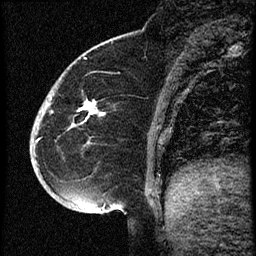
Breast MRI (dynamic contrast-enhanced), one sagittal slice; position 17 of 60 along the scan axis; dynamic contrast-enhanced study with each time point stored as its own series, time point 2 of 3 at this slice position (early post-contrast, ordered by acquisition time); 1.5 T; TE 4.2 ms, TR 18.9 ms; 256 × 256 image matrix, field of view 200 × 200 mm. Female patient. Case-level facts recorded for this patient, not image findings: setting: breast cancer imaged before/during neoadjuvant chemotherapy; receptor status: HR-positive, HER2-negative.
Annotated regions visible in this slice (semi-automatically segmented with operator editing):
- analysis volume of interest (the breast-tissue region the enhancement analysis was run in; not a lesion): bounding box <31,87,108,173> (left, top, right, bottom; pixels)
- tumour enhancement mask (voxels above the 100 % enhancement threshold inside the analysis volume of interest): <87,104,103,116>